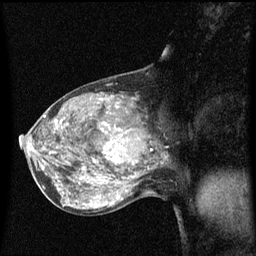
Breast MRI (dynamic contrast-enhanced), one sagittal slice; slice 30 of 60 in the series (ordered by position); dynamic contrast-enhanced series, image 2 of 3 at this slice position (ordered by acquisition); 1.5 T; TE 4.2 ms, TR 8.4 ms; 256 × 256 image matrix, field of view 200 × 200 mm. Female patient, age 50 years.
Annotated regions visible in this slice (semi-automatic segmentation, software-assisted and operator-edited):
- analysis volume of interest (the breast-tissue region the enhancement analysis was run in; not a lesion): bounding box (x1, y1, x2, y2) in pixels: (100, 114, 153, 171)
- tumour enhancement mask (voxels above the 70 % enhancement threshold inside the analysis volume of interest): (100, 122, 120, 169)